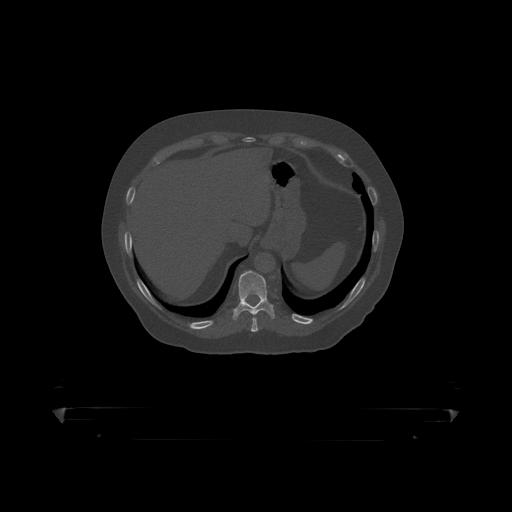
CT including the spine, one axial slice; slice 218 of 390 in the series (ordered by position); 120 kVp; bone window (W 1800 / L 400 HU); 1.25 mm slice thickness; 512 × 512 image matrix. Patient: male, 60 years. Case-level facts recorded for this patient, not image findings: primary cancer: prostate.
Annotated regions visible in this slice (semi-automatic segmentation, software-assisted and operator-edited):
- T10 vertebra: box from (x=233, y=271) to (x=275, y=317) px
- T9 vertebra: (x=253, y=317)–(x=257, y=319)